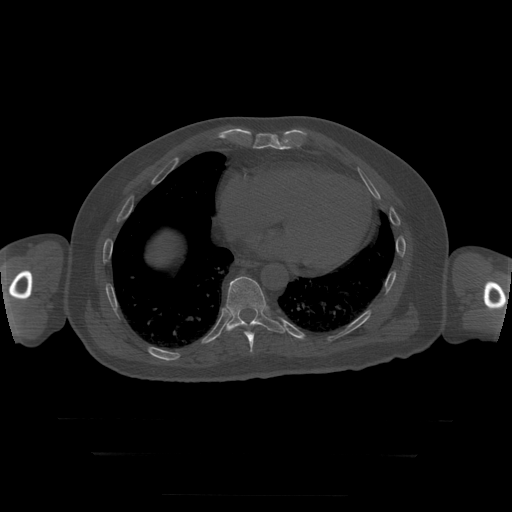
CT including the spine, one axial slice; slice 130 of 397 in the series (ordered by position); reconstruction kernel STANDARD; 120 kVp; bone window (W 1800 / L 400 HU); 1.25 mm slice thickness; 512 × 512 image matrix, field of view 510 × 510 mm. Patient age 73 years. From the clinical record (not read from this slice): primary cancer: prostate.
Outlined on this slice (semi-automatic segmentation, software-assisted and operator-edited):
- T10 vertebra: bounding box <226,277,286,334> (left, top, right, bottom; pixels)
- T9 vertebra: <245,331,254,353>